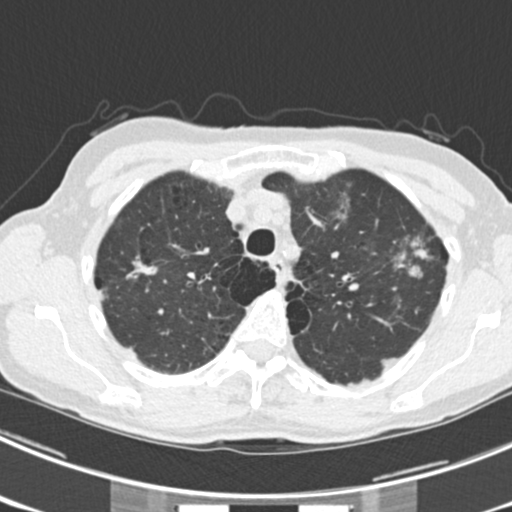
Low-dose screening chest CT, one axial slice. Position 175 of 225 along the scan axis. Reconstruction kernel B30f. 120 kVp. Lung window (W 1500 / L -600 HU). 2 mm slice thickness. 512 × 512 image matrix, field of view 302 × 302 mm.
Annotated regions visible in this slice (outlined manually by an expert reader):
- lesion 1 (tumor, upper lobe of left lung): box from (x=408, y=237) to (x=431, y=279) px
- lesion 5 (tumor, upper lobe of right lung): (x=129, y=258)–(x=159, y=279)